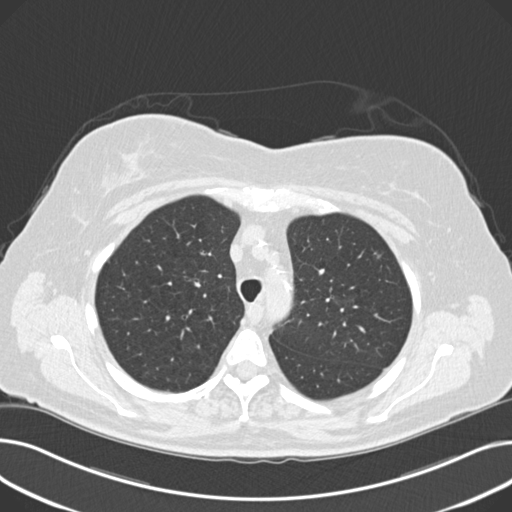
Chest CT (low-dose screening protocol), one axial image. Third annual screen. Lung window (W 1500 / L -600 HU). Standard (soft-tissue) reconstruction kernel (B30f). Slice 56 of 203 in the series. 512 × 512 image matrix, field of view 372 × 372 mm. Female participant, aged 60 years at enrolment. Current smoker at enrolment.
Expert-annotated lung lesion, box from (x=359, y=239) to (x=406, y=279) px. The screening reader recorded 8 non-calcified nodules or masses ≥4 mm on this exam (right upper lobe, lingula, lingula, right middle lobe, right lower lobe, left lower lobe, left lower lobe, left lower lobe); which of them this box marks is not recorded. Official screen result: positive, other. Lung cancer was diagnosed 176 days after this screen: non-small cell carcinoma, left upper lobe, poorly differentiated (G3), stage IB (AJCC 6th edition), 7 mm at pathology.